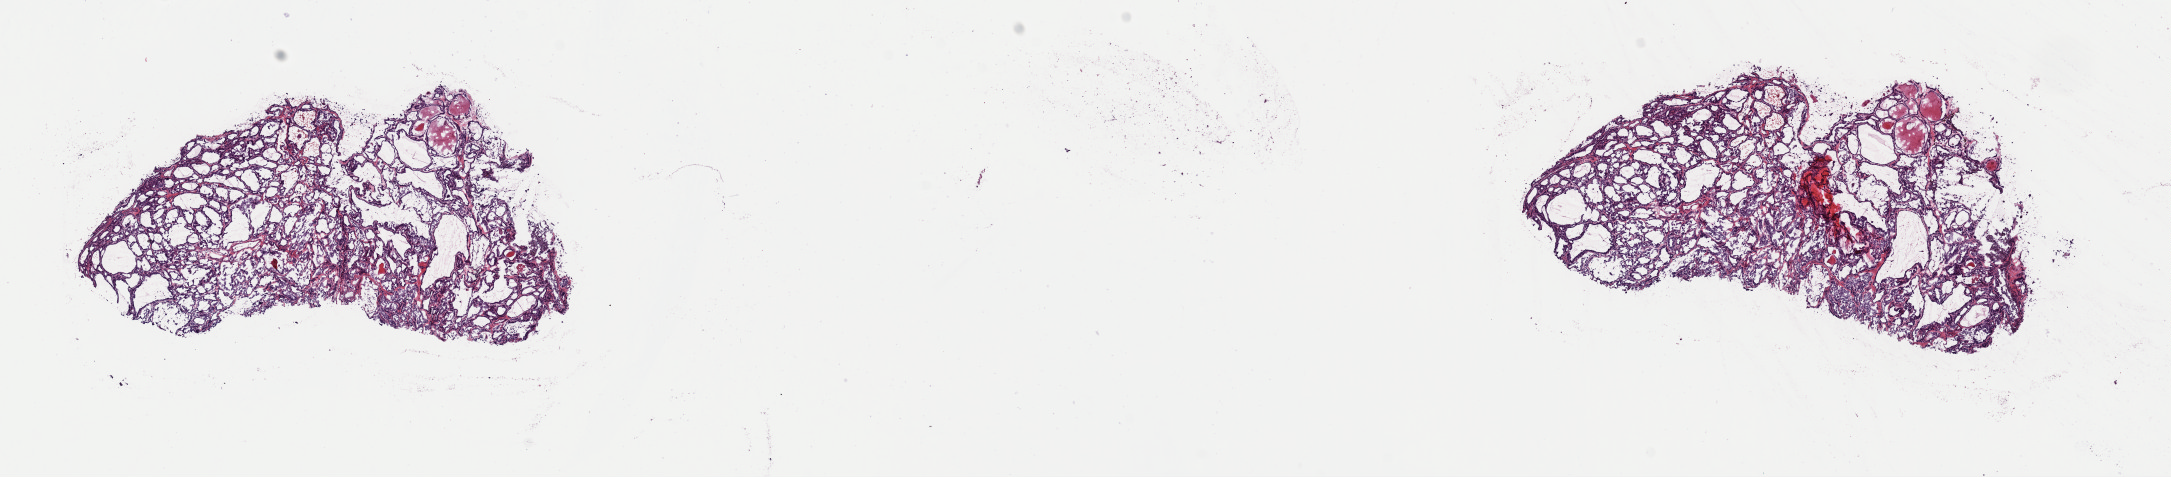
Digitized H&E-stained tissue section (whole slide), low-resolution overview of the scanned area, about 17.2 x 3.8 mm; frozen section; sample: primary tumour, thyroid. Female, age 43 years at initial diagnosis. Composition of this section per pathologist review: tumour cells 100%, tumour nuclei 80%, normal cells 0%, stromal cells 0%, necrosis 0%. Infiltration values recorded for this section: lymphocyte infiltration 2%, monocyte infiltration 0%, neutrophil infiltration 0%.
AJCC pathologic stage: I (7th edition). TNM: T1 N0 M0. Laterality: left. Lymph nodes positive (case pathology): 0 of 1 examined. Diagnosis: Papillary adenocarcinoma, NOS (thyroid gland).